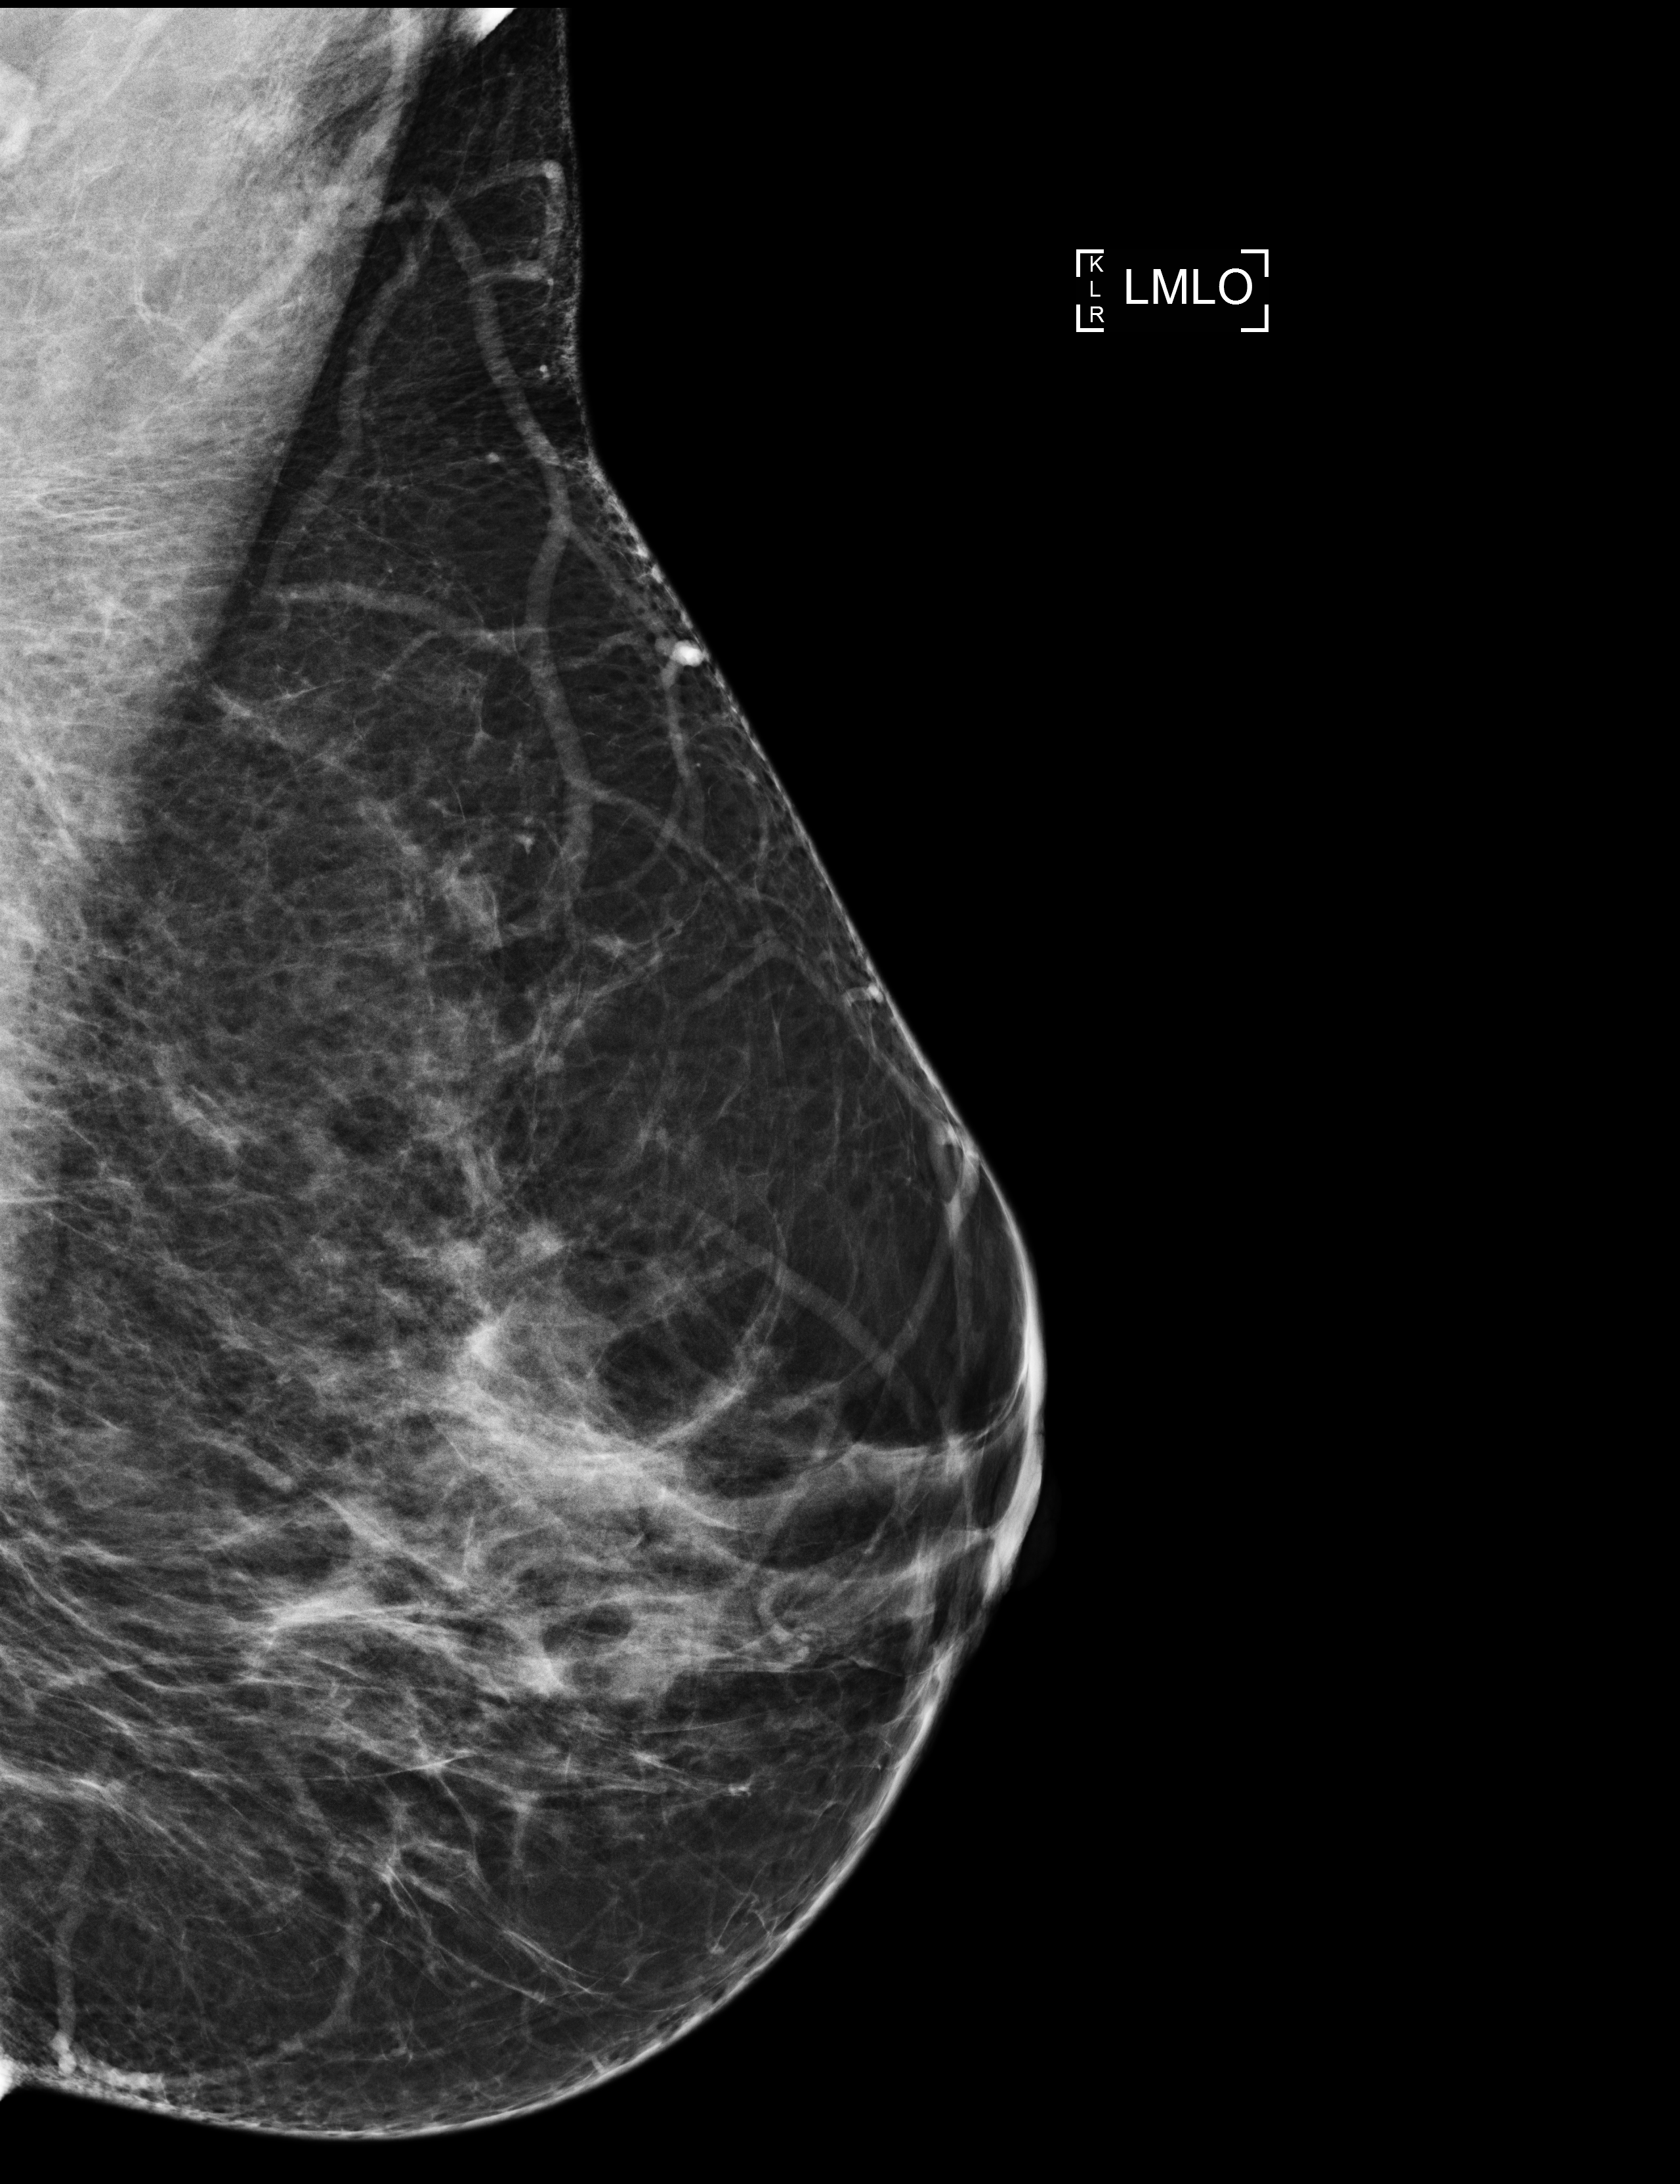
Digital mammogram (FFDM), left breast, medio-lateral oblique projection, screening examination, compressed breast thickness 75 mm. Patient aged 47 years (female).
BI-RADS breast density category at the screening exam (both breasts, scale 1–4): 2. Final BI-RADS category for the screening round (tomosynthesis exam, both breasts): category 1. Recall: no recall after this screen.